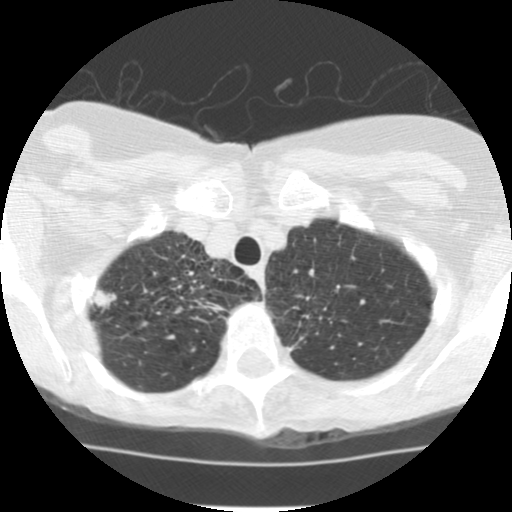
Low-dose screening chest CT, axial slice; baseline annual screen; lung window (W 1500 / L -600 HU); 2.5 mm slice thickness; standard (soft-tissue) reconstruction kernel (STANDARD); slice 23 of 135 in the series. Female, age 68 years at enrolment.
Expert reader's lesion annotation, bounding box (x1, y1, x2, y2) in pixels: (73, 273, 131, 330). The screening reader recorded 2 non-calcified nodules or masses ≥4 mm on this exam (right upper lobe, right upper lobe); which of them this box marks is not recorded. Participant outcome: lung cancer diagnosed 411 days after this screen (after the second annual screen) — large cell neuroendocrine carcinoma, right upper lobe, undifferentiated (G4), stage IB (AJCC 6th edition), 22 mm at pathology.